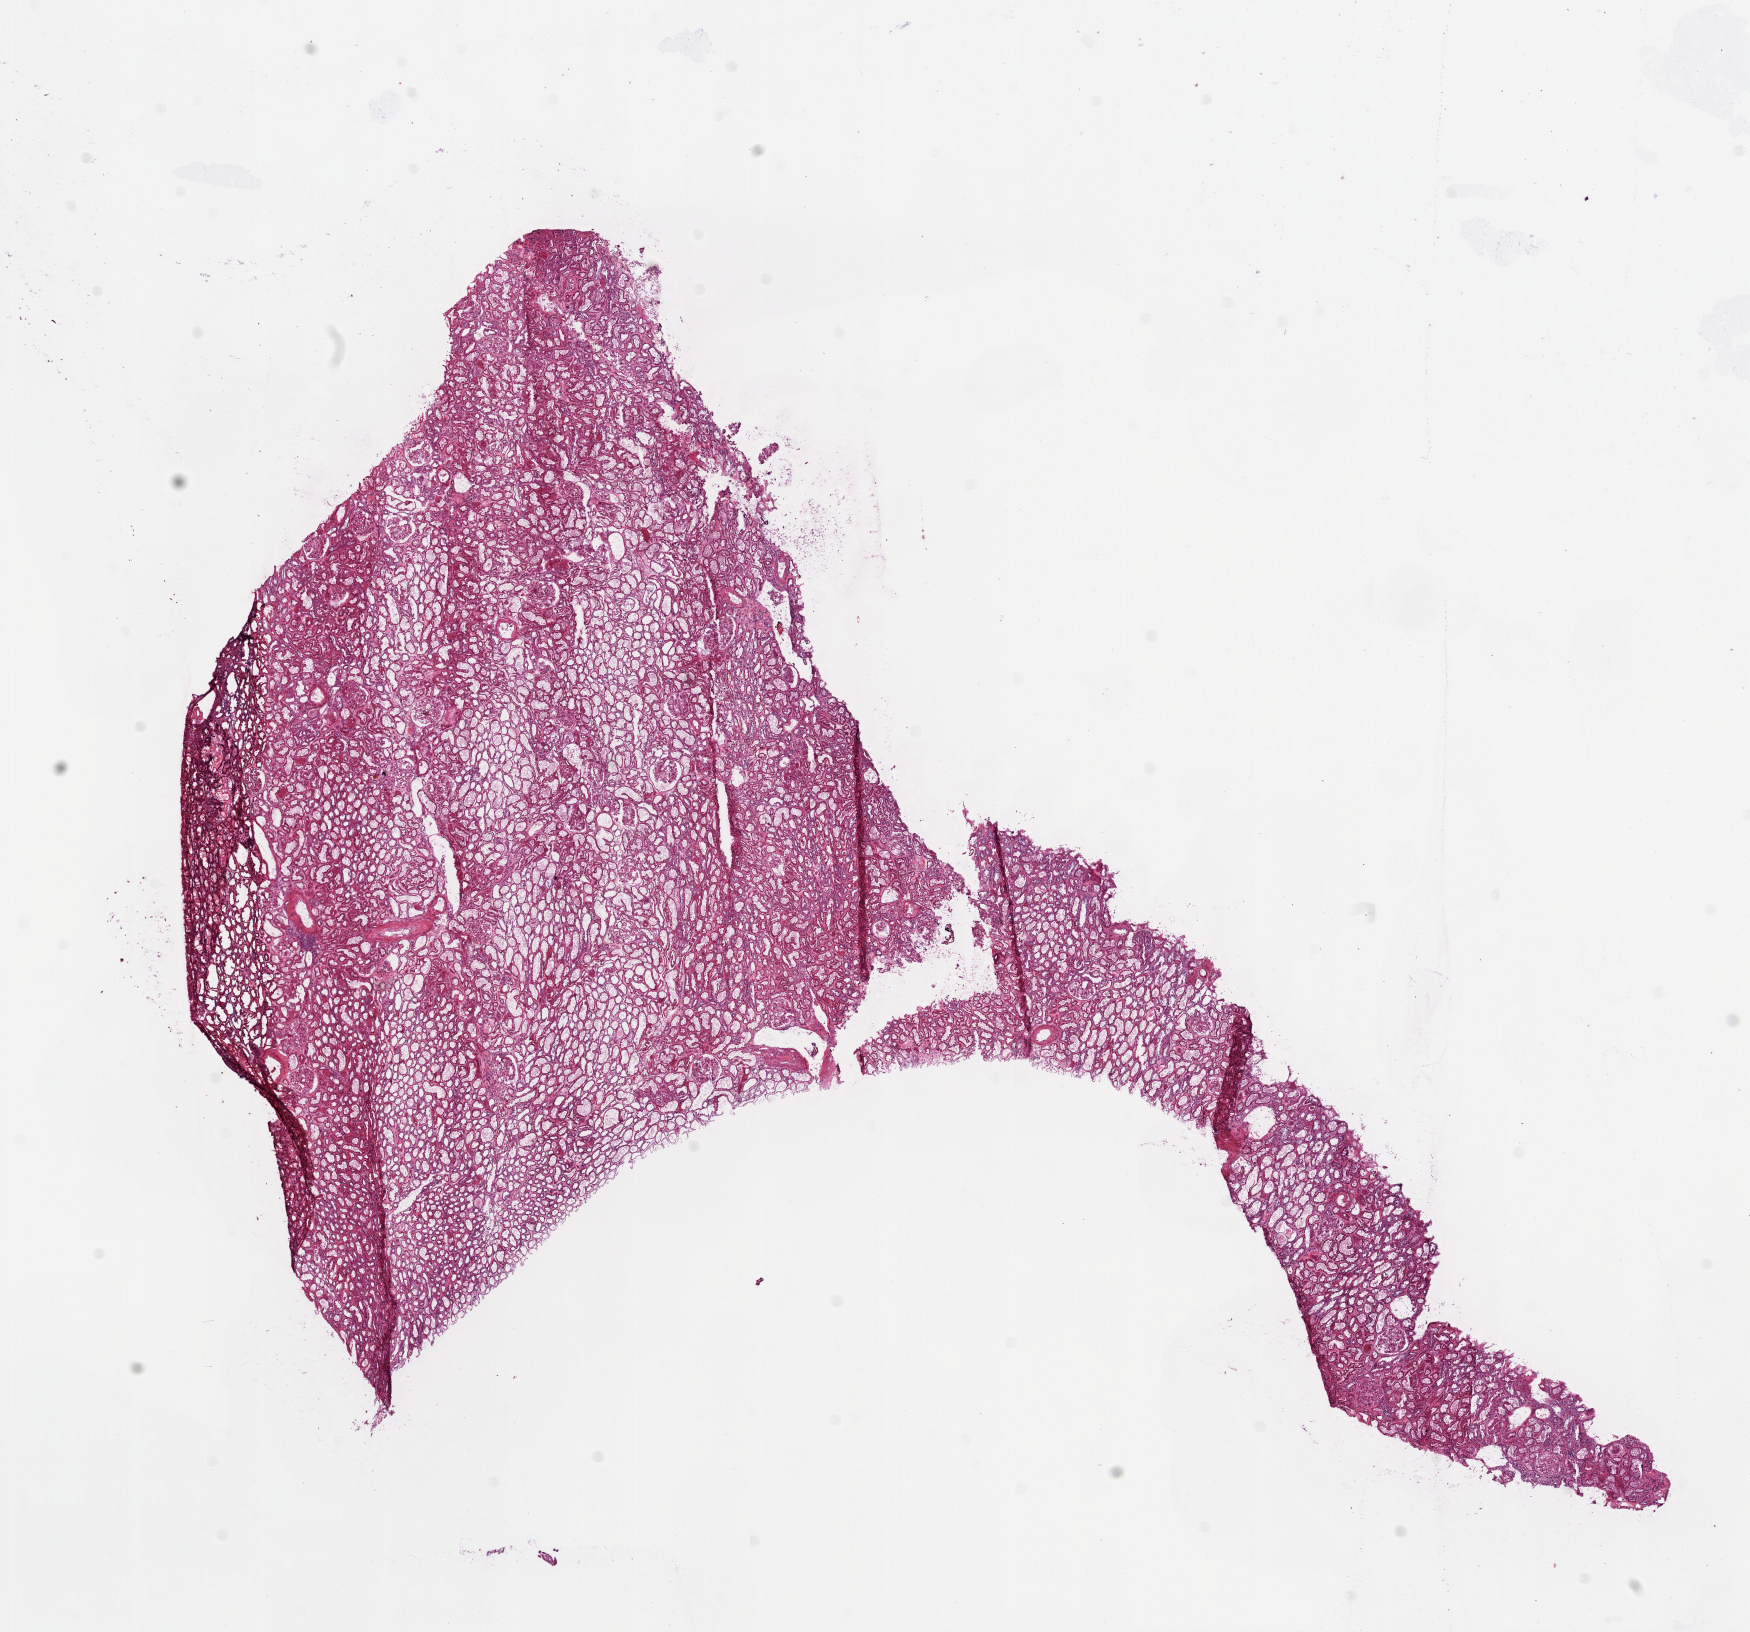
Digitized H&E-stained tissue section (whole slide) — a low-resolution overview of the entire scanned area, about 14.0 x 13.1 mm, frozen section from the bottom of the tissue portion, sample: solid tissue normal (non-tumour tissue), kidney. Male patient; age at initial diagnosis 67 years.
- this section: solid tissue normal (non-tumour) sample from the same patient
- patient diagnosis: Clear cell adenocarcinoma, NOS